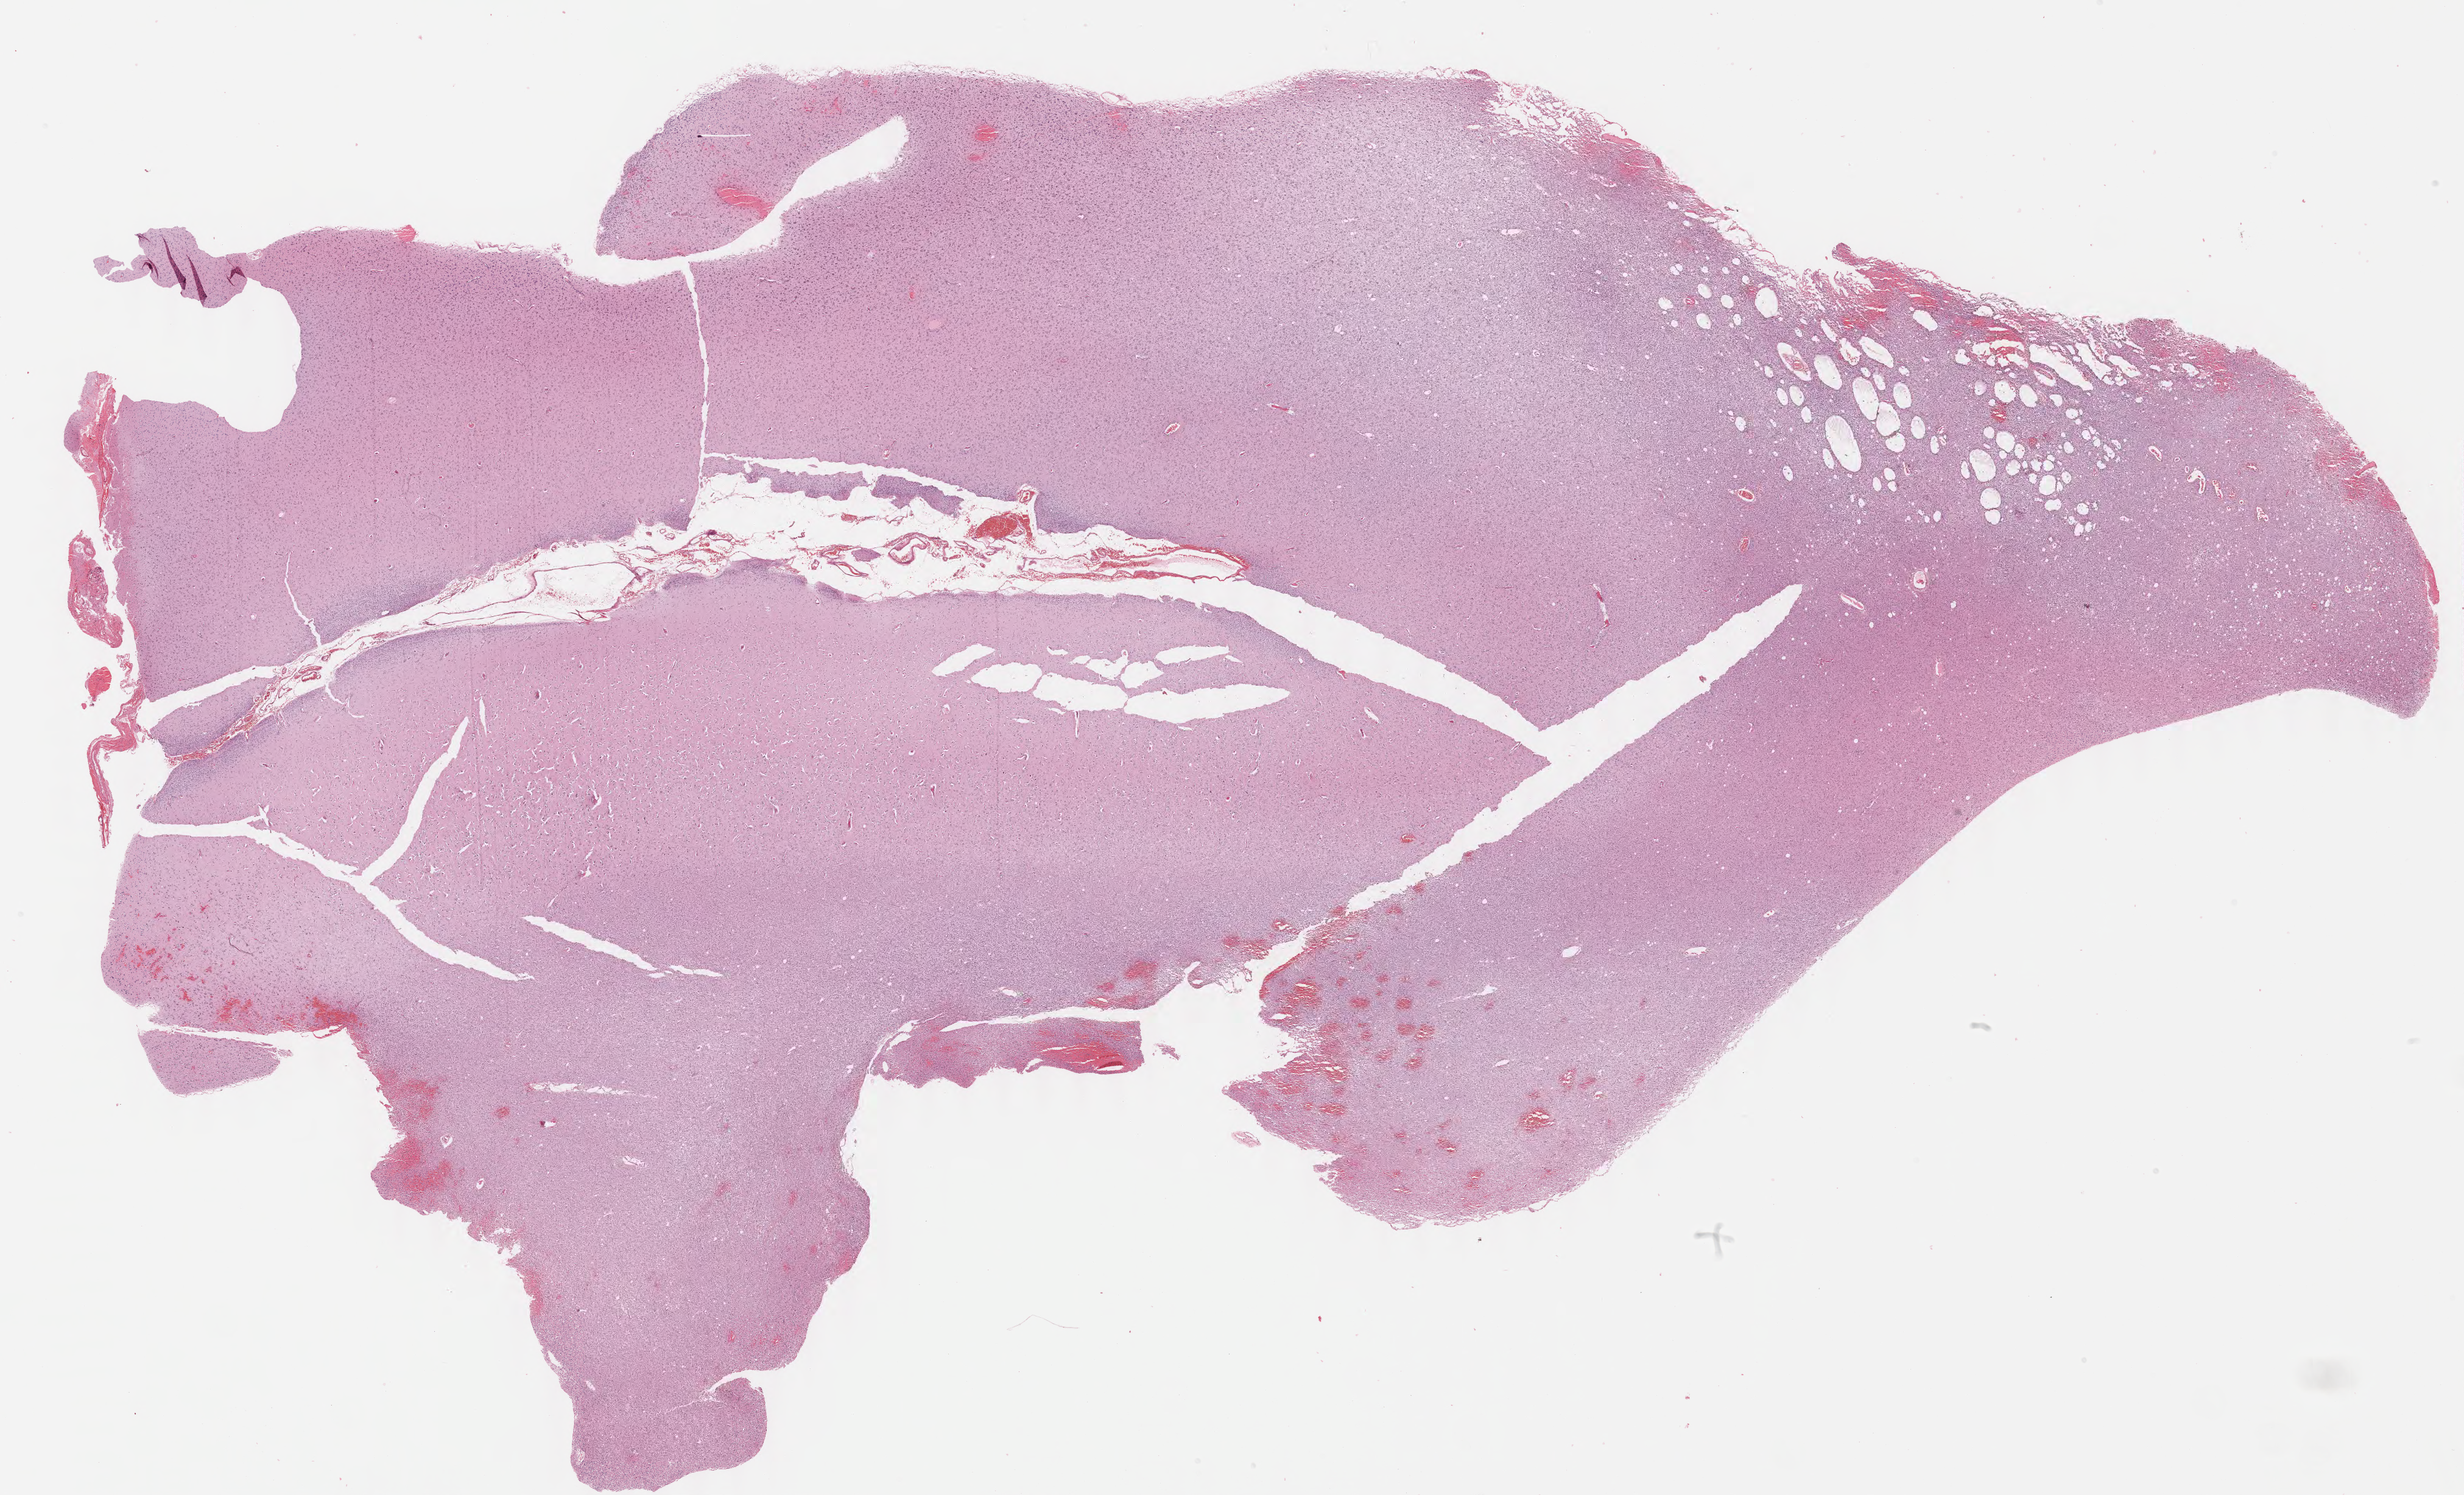
Digitized H&E tissue section (whole slide) — shown as a low-resolution overview of the whole scanned area (about 32.0 x 19.4 mm, from a 40x scan), formalin-fixed paraffin-embedded (FFPE) diagnostic section, brain, primary tumour sample. Patient: female, age at initial diagnosis 38 years. Histologic grade: G2 (moderately differentiated).
Histologic diagnosis: Mixed glioma (cerebrum).